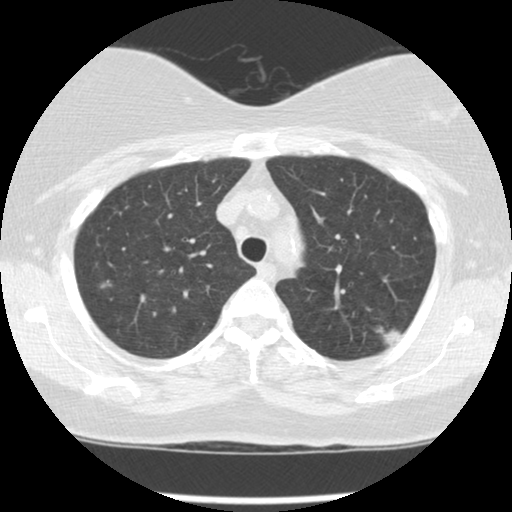
Low-dose screening chest CT, axial slice, third screening round (two years after baseline), lung window (W 1500 / L -600 HU), 2.5 mm slice thickness, slice 26 of 127 in the series, 512 × 512 image matrix. Female participant, aged 56 years at enrolment. Current smoker at enrolment.
Expert reader's lesion annotation, bounding box [x1, y1, x2, y2] px = [341, 304, 417, 366]. The screening reader recorded 4 non-calcified nodules or masses ≥4 mm on this exam (left upper lobe, left upper lobe, left upper lobe, right upper lobe); which of them this box marks is not recorded. Participant outcome: lung cancer diagnosed 49 days after this screen — adenocarcinoma, NOS, left upper lobe, moderately differentiated (G2), stage IA (AJCC 6th edition), 10 mm at pathology.